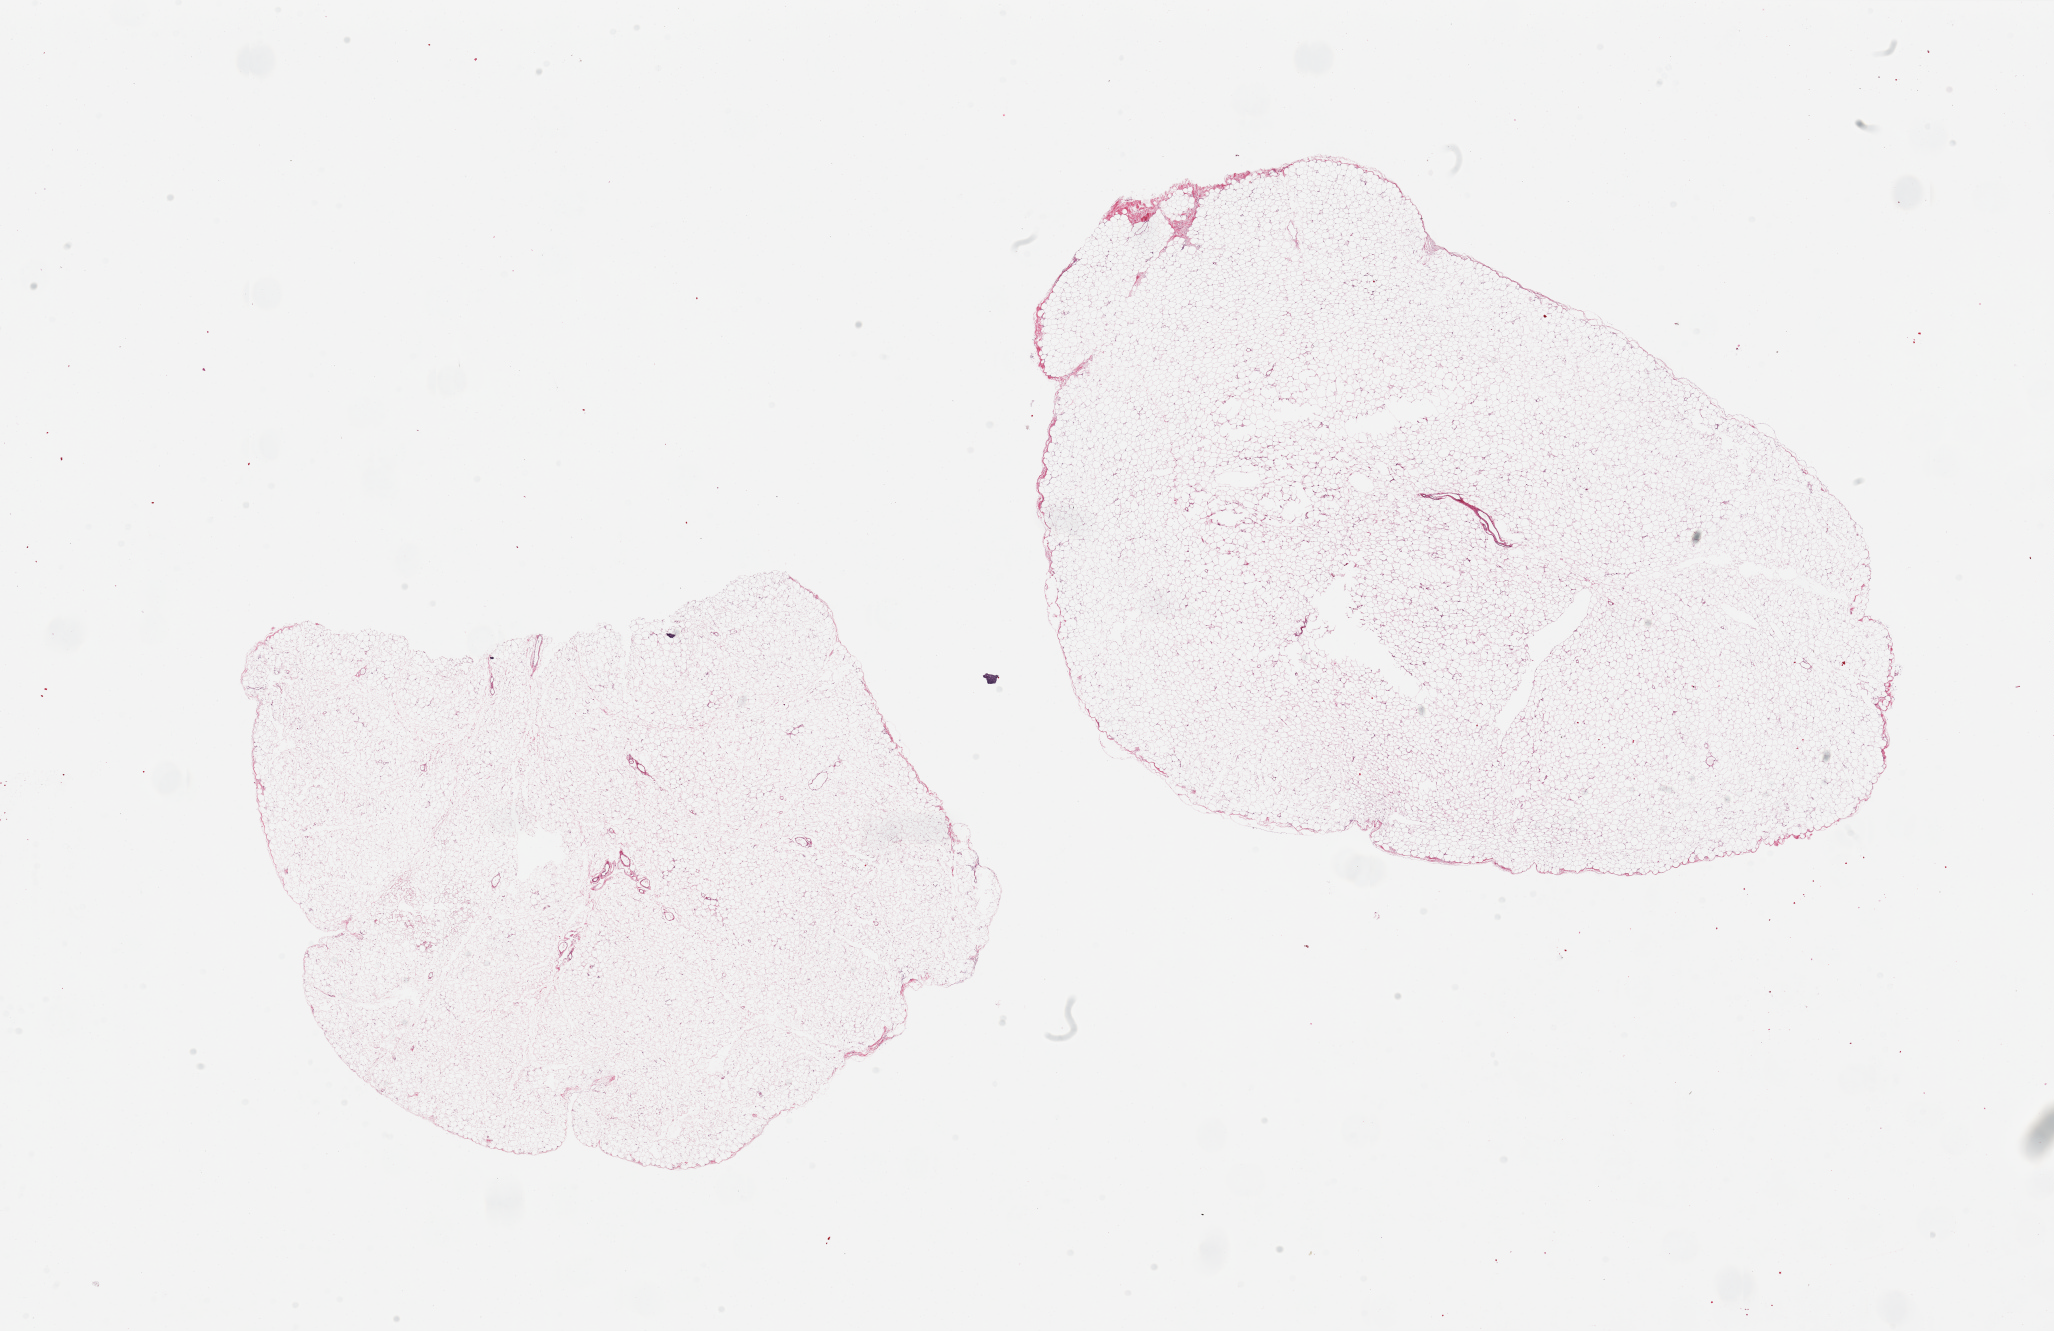
Digitized H&E-stained section — shown as a low-resolution overview of the whole scanned area (about 32.5 x 21.1 mm), PAXgene-fixed paraffin-embedded (PFPE) section, sampled site (target tissue): omentum, donor tissue sample. Donor sex: female.
Reviewer comment on this tissue sample: 2 pieces. Large size needed refixing.